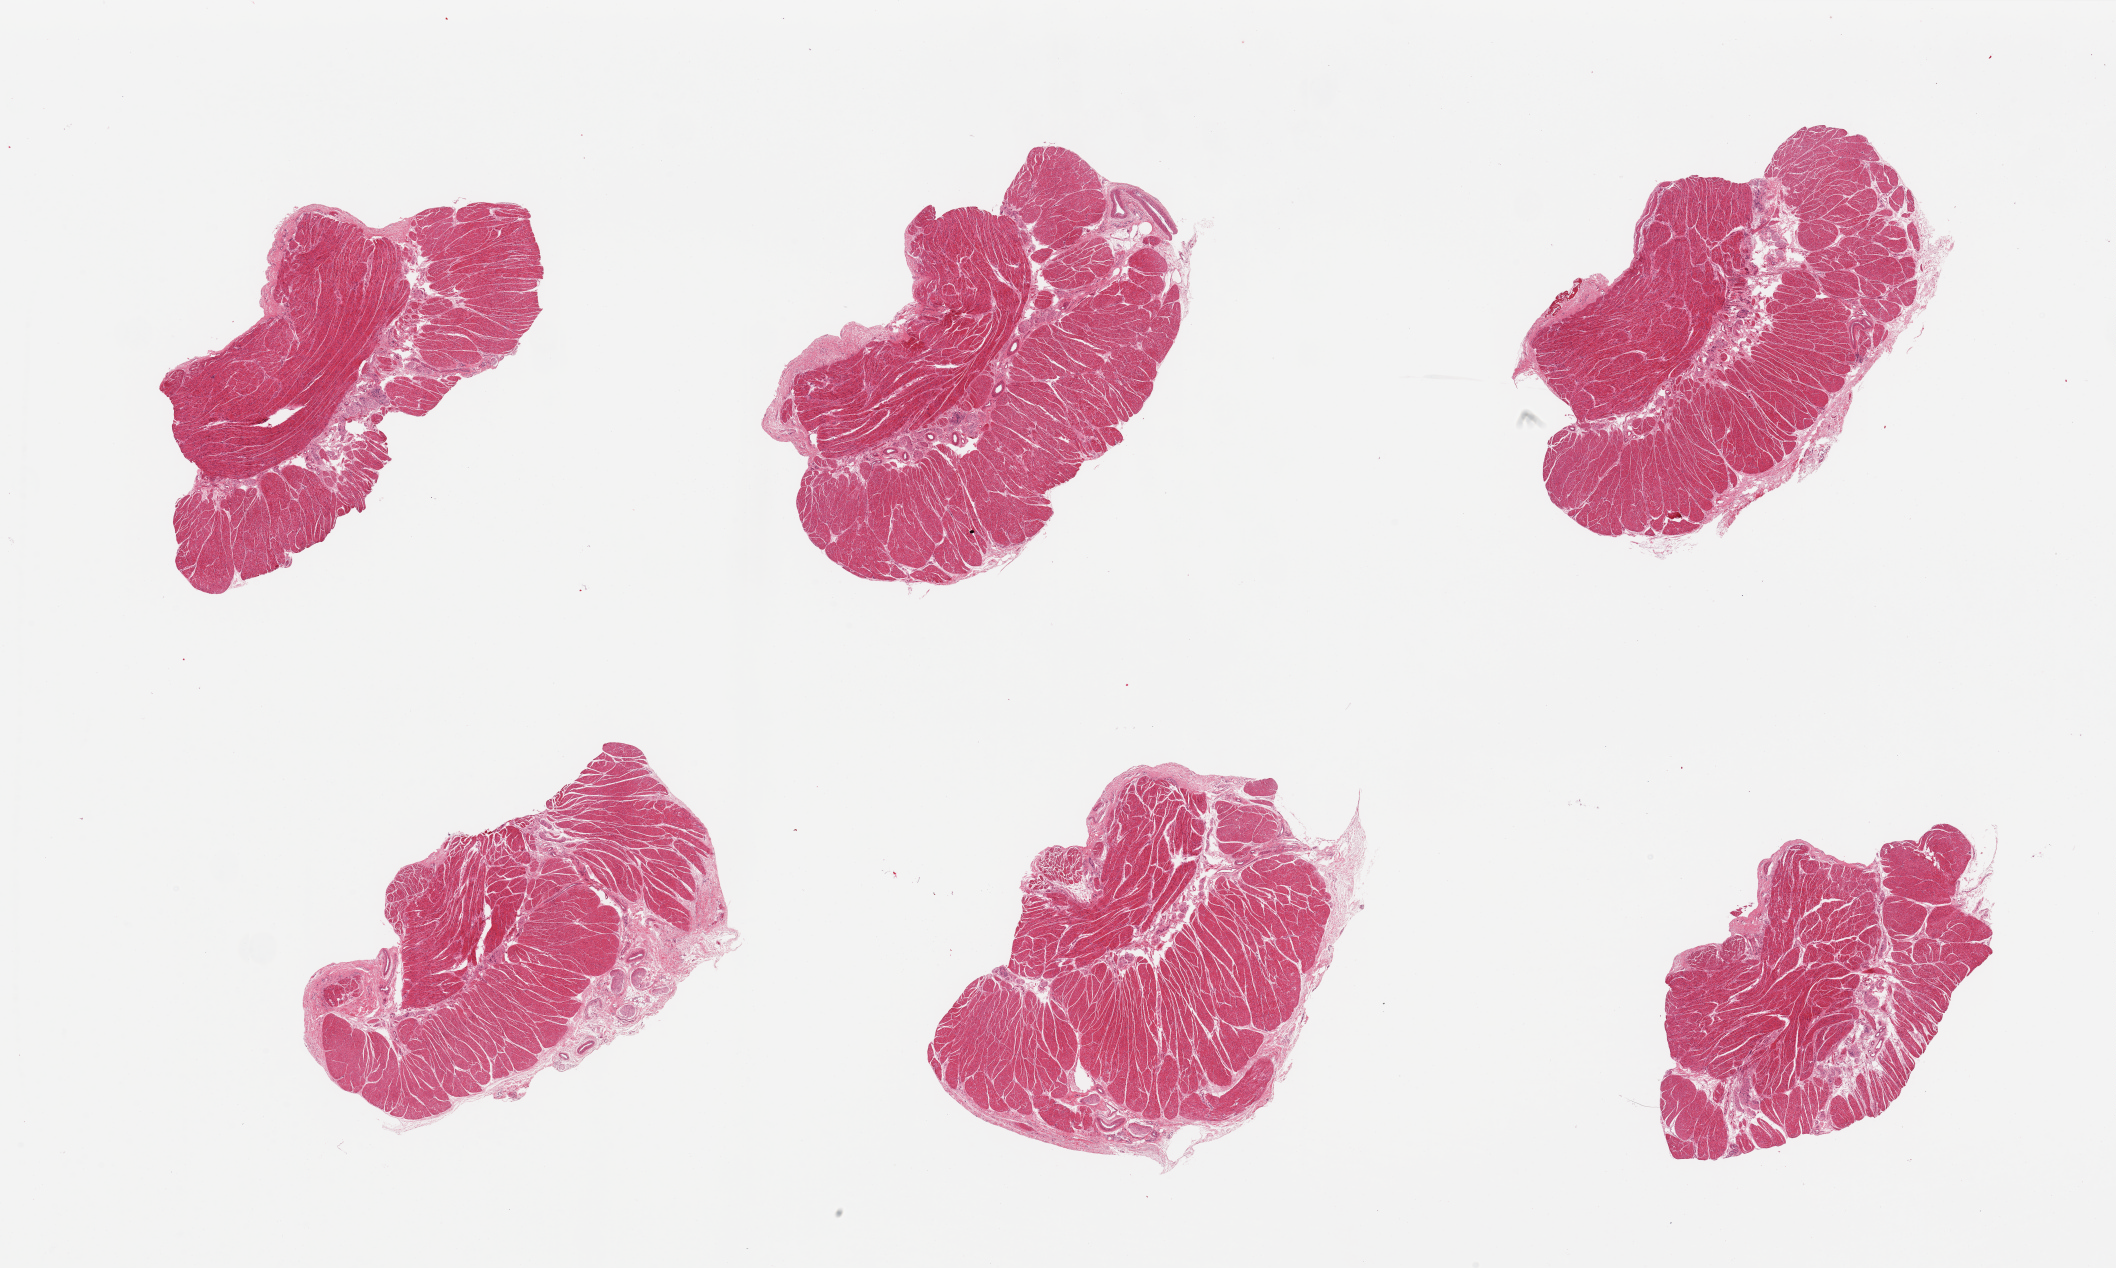
Digitized hematoxylin and eosin (H&E)-stained section — whole scanned area (about 33.5 x 20.1 mm) shown as a low-resolution overview. PAXgene-fixed paraffin-embedded (PFPE) section. Section of gastroesophageal junction (target tissue). Donor tissue sample. Donor sex: female.
Pathologist's review note for this sample: 6 pieces, a few with trace adherent fibrous tissue; good specimens.